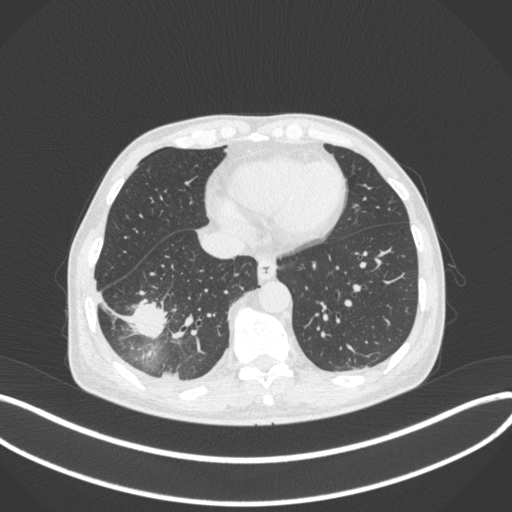
Chest CT, one axial slice; slice 107 of 385 in the series (ordered by position); 120 kVp; lung window (W 1500 / L -600 HU); 1 mm slice thickness; 512 × 512 image matrix, field of view 400 × 400 mm. Patient: male, 64 years. Case-level facts recorded for this patient, not image findings: clinical TNM (as recorded): T3 N0 M0.
Annotated regions visible in this slice (bounding box drawn by a radiologist):
- lung tumour (recorded histology: adenocarcinoma): bounding box (x1, y1, x2, y2) in pixels: (123, 289, 169, 343)